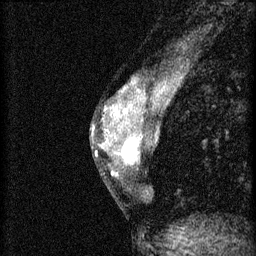
Breast MRI (dynamic contrast-enhanced), one sagittal slice. Position 25 of 46 along the scan axis. 3 images stored at this slice position (order not interpretable as contrast timing). 1.5 T. TE 4.2 ms, TR 8.2 ms. 2 mm slice thickness. 256 × 256 image matrix, field of view 180 × 180 mm. Female patient, age 44 years.
Annotated regions visible in this slice (semi-automatically segmented with operator editing):
- analysis volume of interest (the breast-tissue region the enhancement analysis was run in; not a lesion): bounding box [x1, y1, x2, y2] px = [110, 128, 156, 179]
- tumour enhancement mask (voxels above the 70 % enhancement threshold inside the analysis volume of interest): [112, 134, 144, 177]